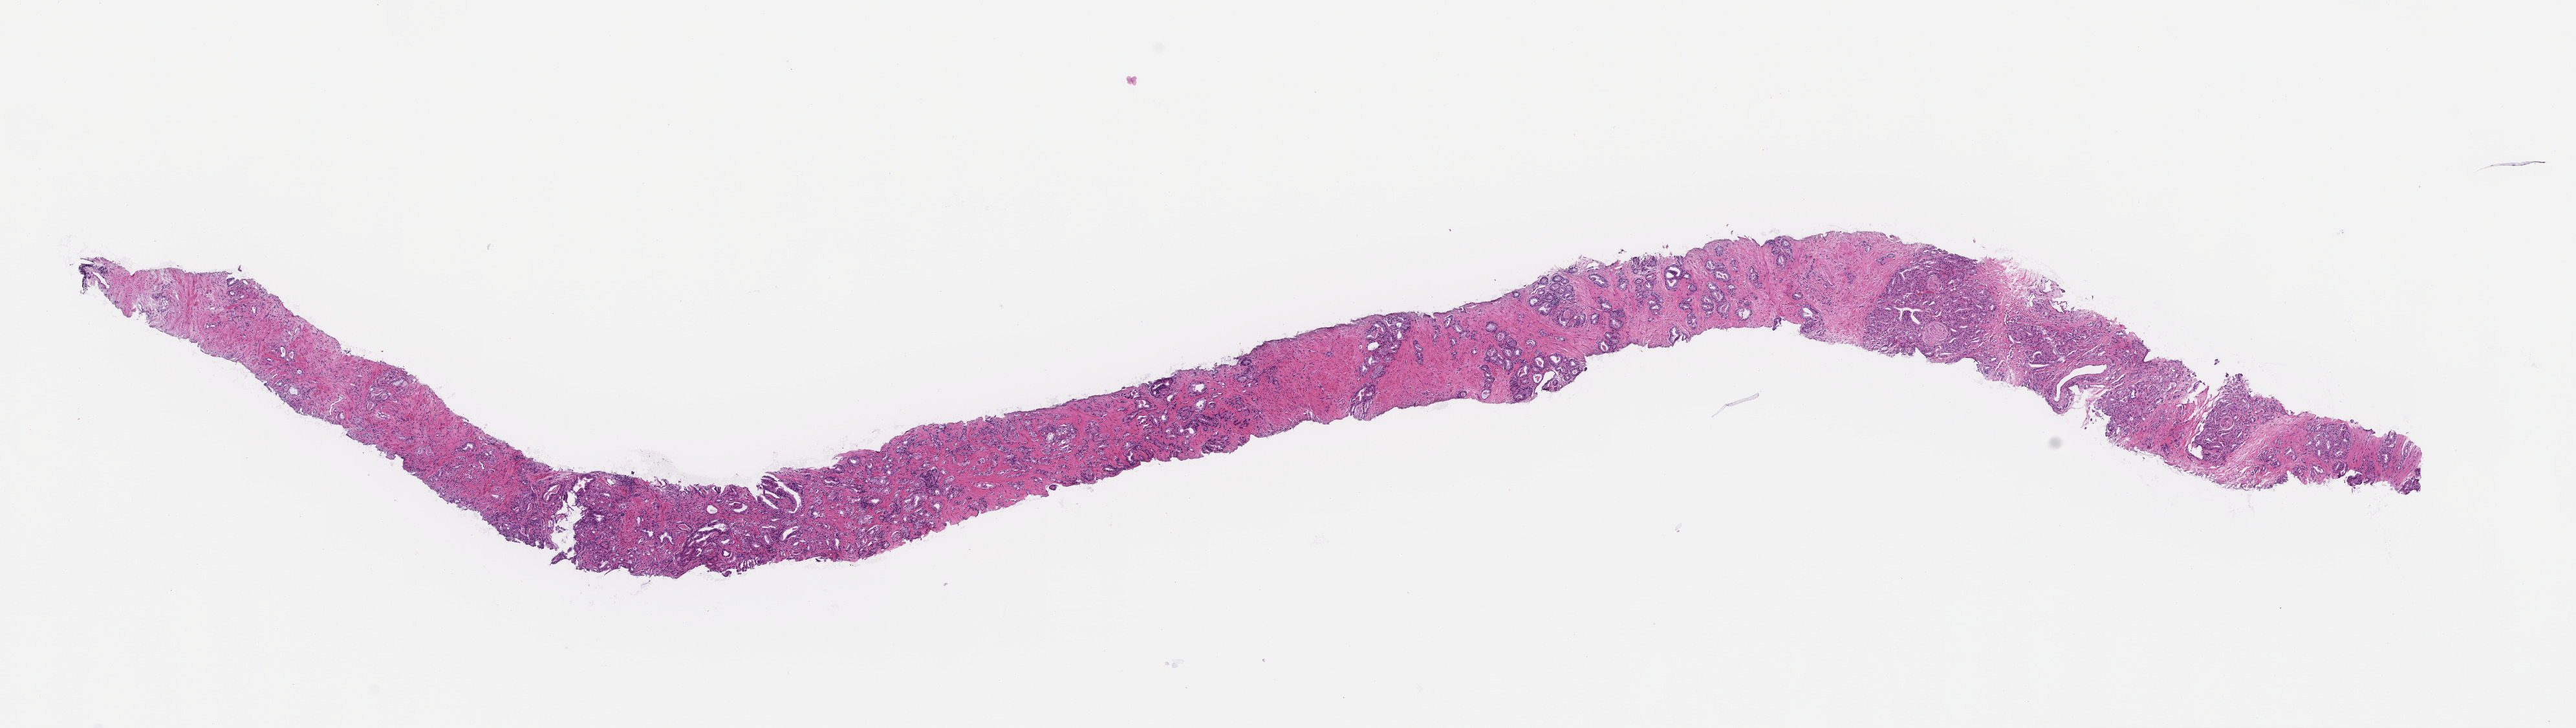
Digitized H&E-stained section — a low-resolution overview of the entire scanned area, about 16.1 x 4.5 mm; formalin-fixed, paraffin-embedded (FFPE) tissue; site: prostate; archival tissue. Patient sex: male.
• this section: primary tumour tissue
• diagnosis: Prostate Carcinoma